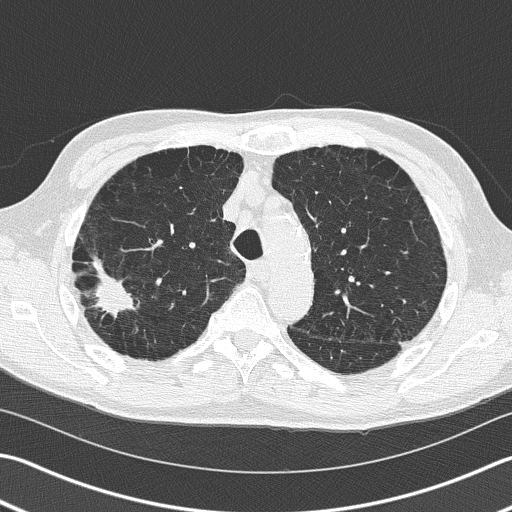
Low-dose screening chest CT, one axial slice; position 116 of 163 along the scan axis; reconstruction kernel B50f; 120 kVp; lung window (W 1500 / L -600 HU); 2 mm slice thickness; 512 × 512 image matrix, field of view 346 × 346 mm.
Structures marked on this image (manually delineated by an expert):
- lesion 1 (tumor, upper lobe of right lung): bounding box (x1, y1, x2, y2) in pixels: (93, 258, 133, 317)